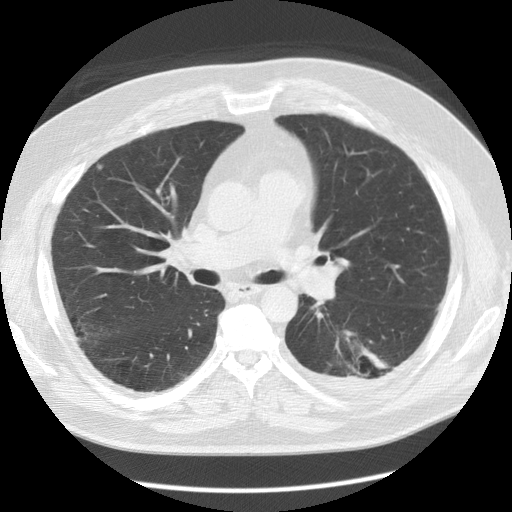
Low-dose screening chest CT, one axial slice. Slice 75 of 126 in the series (ordered by position). 120 kVp. Lung window (W 1500 / L -600 HU). 512 × 512 image matrix, field of view 370 × 370 mm.
Outlined on this slice (outlined manually by an expert reader):
- lesion 1 (tumor, lower lobe of left lung): box from (x=361, y=347) to (x=387, y=368) px